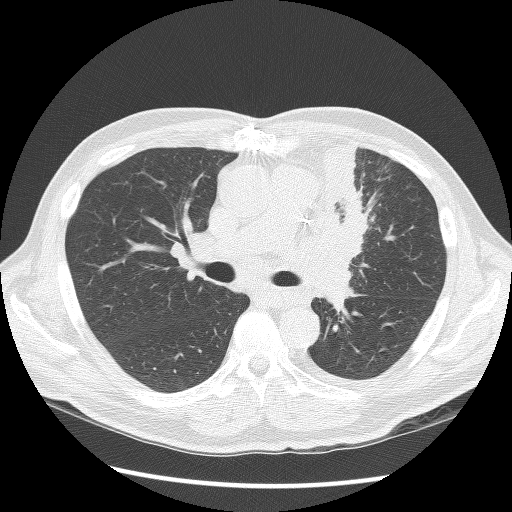
Chest CT (low-dose screening protocol), one axial image; second screening round (one year after baseline); lung window (W 1500 / L -600 HU); 120 kVp; slice 51 of 136 in the series. Male participant, aged 64 years at enrolment. Former smoker at enrolment.
Lesion marked by an expert reader, bounding box (x1, y1, x2, y2) in pixels: (302, 145, 383, 283). No non-calcified nodule or mass ≥4 mm was recorded by the screening reader at this exam. Official screen result: positive, other. Participant outcome: lung cancer diagnosed 24 days after this screen — small cell carcinoma, NOS, left upper lobe, stage IV (AJCC 6th edition), 100 mm at pathology.